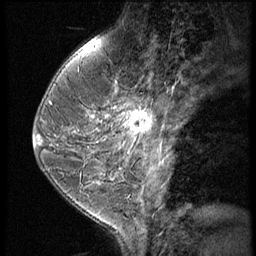
Breast MRI (dynamic contrast-enhanced), one sagittal slice. Slice 23 of 60 in the series (ordered by position). 3 images stored at this slice position (order not interpretable as contrast timing). 1.5 T. TE 4.2 ms, TR 9 ms. 2.5 mm slice thickness. 256 × 256 image matrix. Patient: female, 38 years. From the clinical record (not read from this slice): setting: breast cancer imaged before/during neoadjuvant chemotherapy; receptor status: triple-negative.
Structures marked on this image (semi-automatically segmented with operator editing):
- analysis volume of interest (the breast-tissue region the enhancement analysis was run in; not a lesion): bounding box <119,93,165,150> (left, top, right, bottom; pixels)
- tumour enhancement mask (voxels above the 140 % enhancement threshold inside the analysis volume of interest): <119,103,150,135>